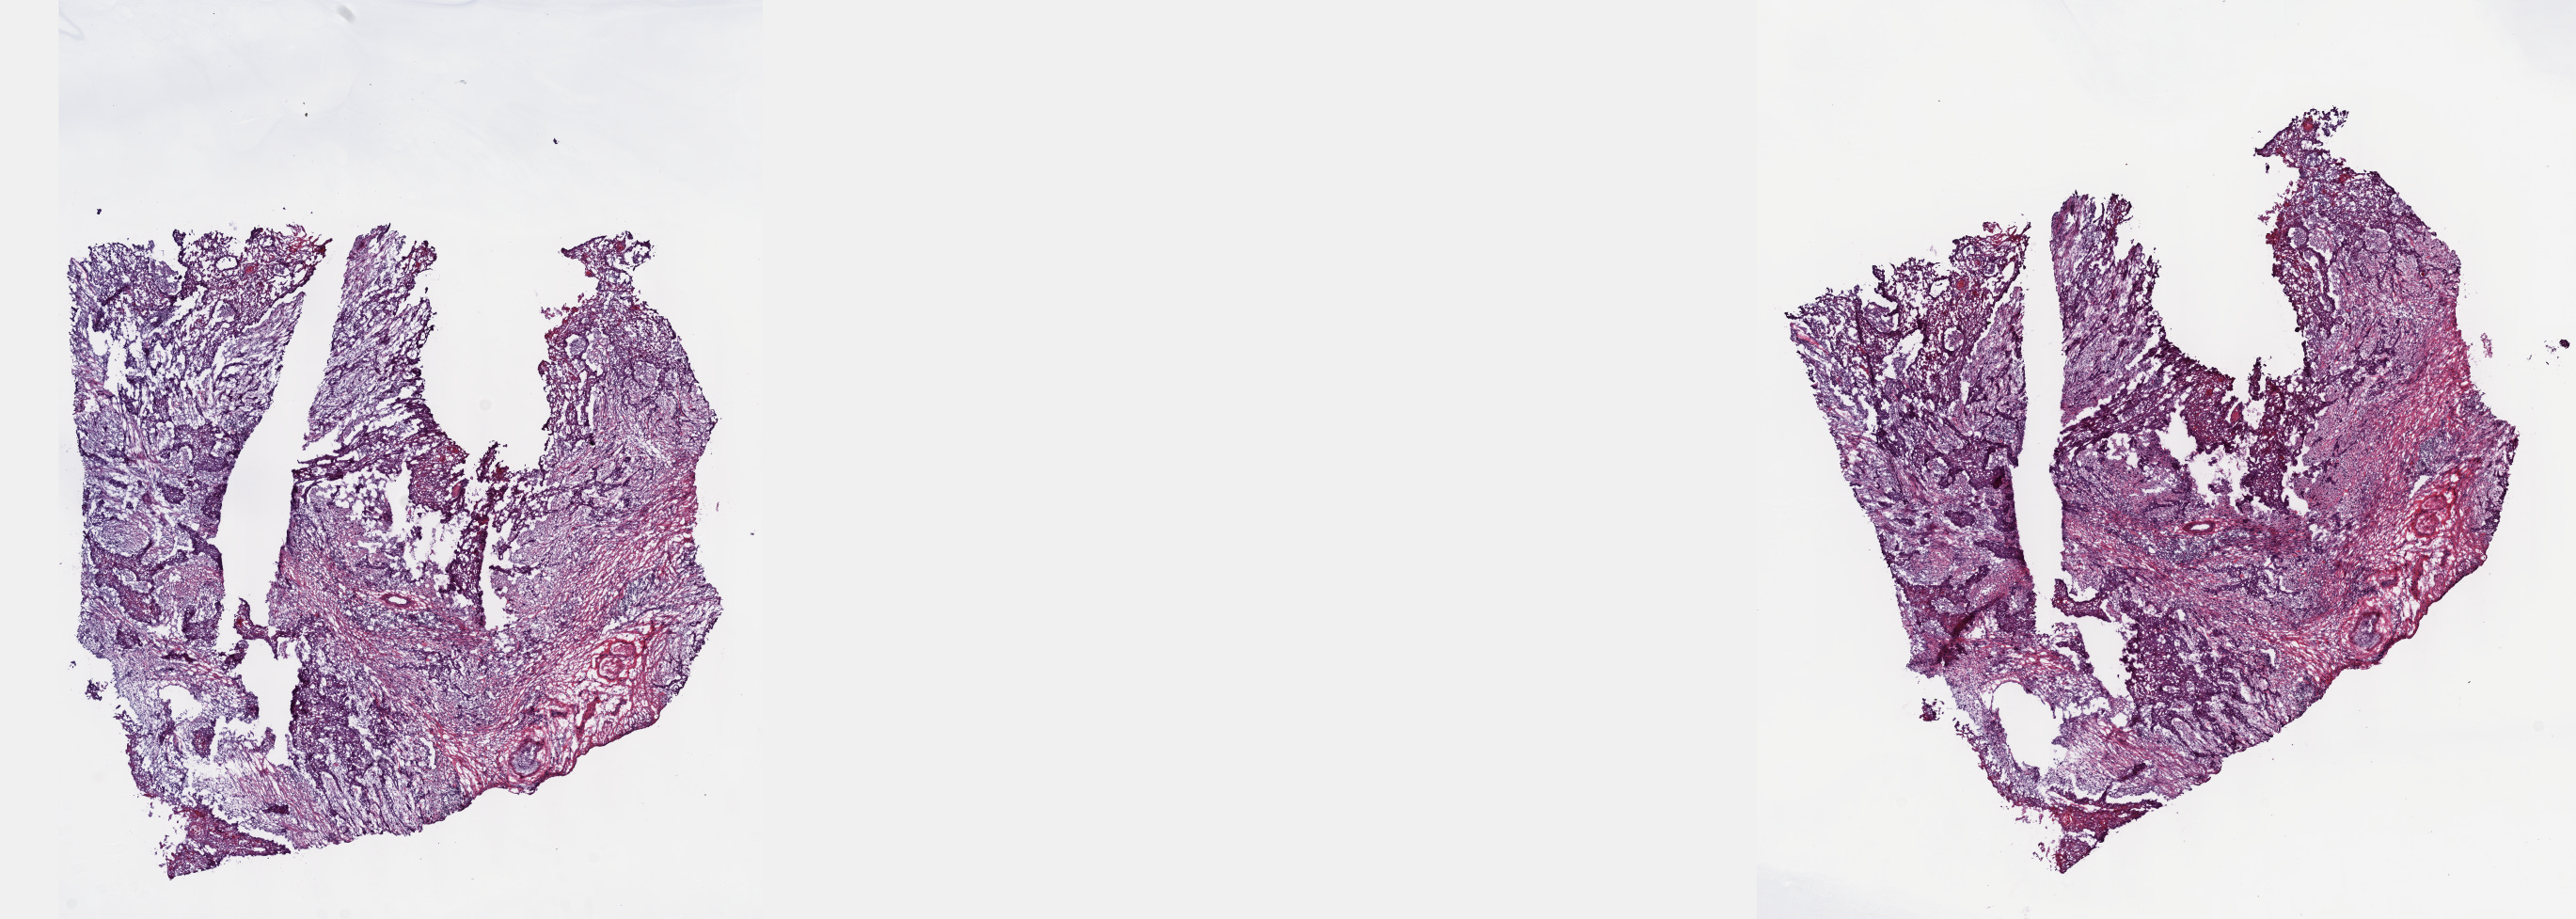
Digitized H&E tissue section (whole slide), a low-resolution overview of the entire scanned area, about 22.1 x 7.9 mm, frozen section from the top of the tissue portion, head and neck, primary tumour sample. Patient: male, age at initial diagnosis 56 years. Histologic grade: G2 (moderately differentiated). Slide review estimates, as recorded: tumour cells 40%, tumour nuclei 60%, normal cells 0%, stromal cells 60%, necrosis 0%. Inflammatory infiltration, as recorded: lymphocyte infiltration 18%, monocyte infiltration 5%, neutrophil infiltration 0%.
Diagnosis: Squamous cell carcinoma, NOS (floor of mouth, NOS). Laterality: right. TNM: T4a N2b M0. Lymph nodes positive (case pathology): 2 of 82 examined. AJCC pathologic stage: IVA (7th edition).